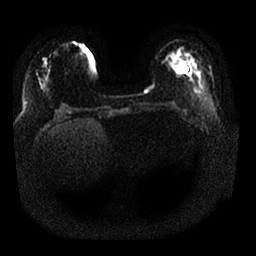
Breast MRI, one axial slice; slice 6 of 25 in the series (ordered by position); diffusion-weighted series; image 2 of 4 stored at this slice position (different b-values; order by instance number); 1.5 T; 256 × 256 image matrix. Female patient.
Outlined on this slice (manually delineated by an expert):
- tumour on diffusion-weighted imaging: bounding box <169,51,186,72> (left, top, right, bottom; pixels)